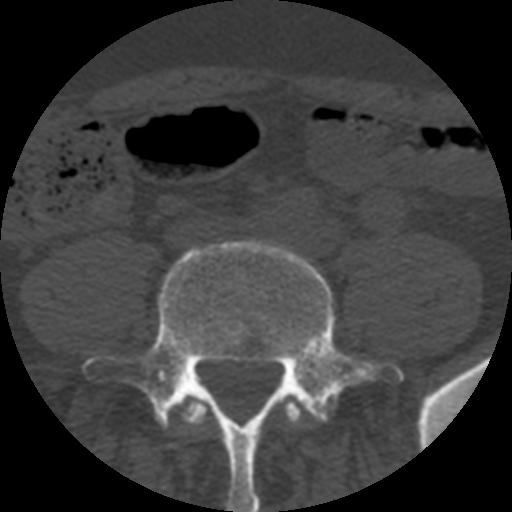
CT including the spine, one axial slice; slice 70 of 508 in the series (ordered by position); reconstruction kernel STANDARD; 120 kVp; bone window (W 1800 / L 400 HU); 512 × 512 image matrix, field of view 160 × 160 mm. Patient age 57 years. Case-level facts recorded for this patient, not image findings: primary cancer: prostate.
Outlined on this slice (semi-automatic segmentation, software-assisted and operator-edited):
- L4 vertebra: bounding box [x1, y1, x2, y2] px = [181, 397, 301, 426]
- L5 vertebra: [83, 241, 403, 512]